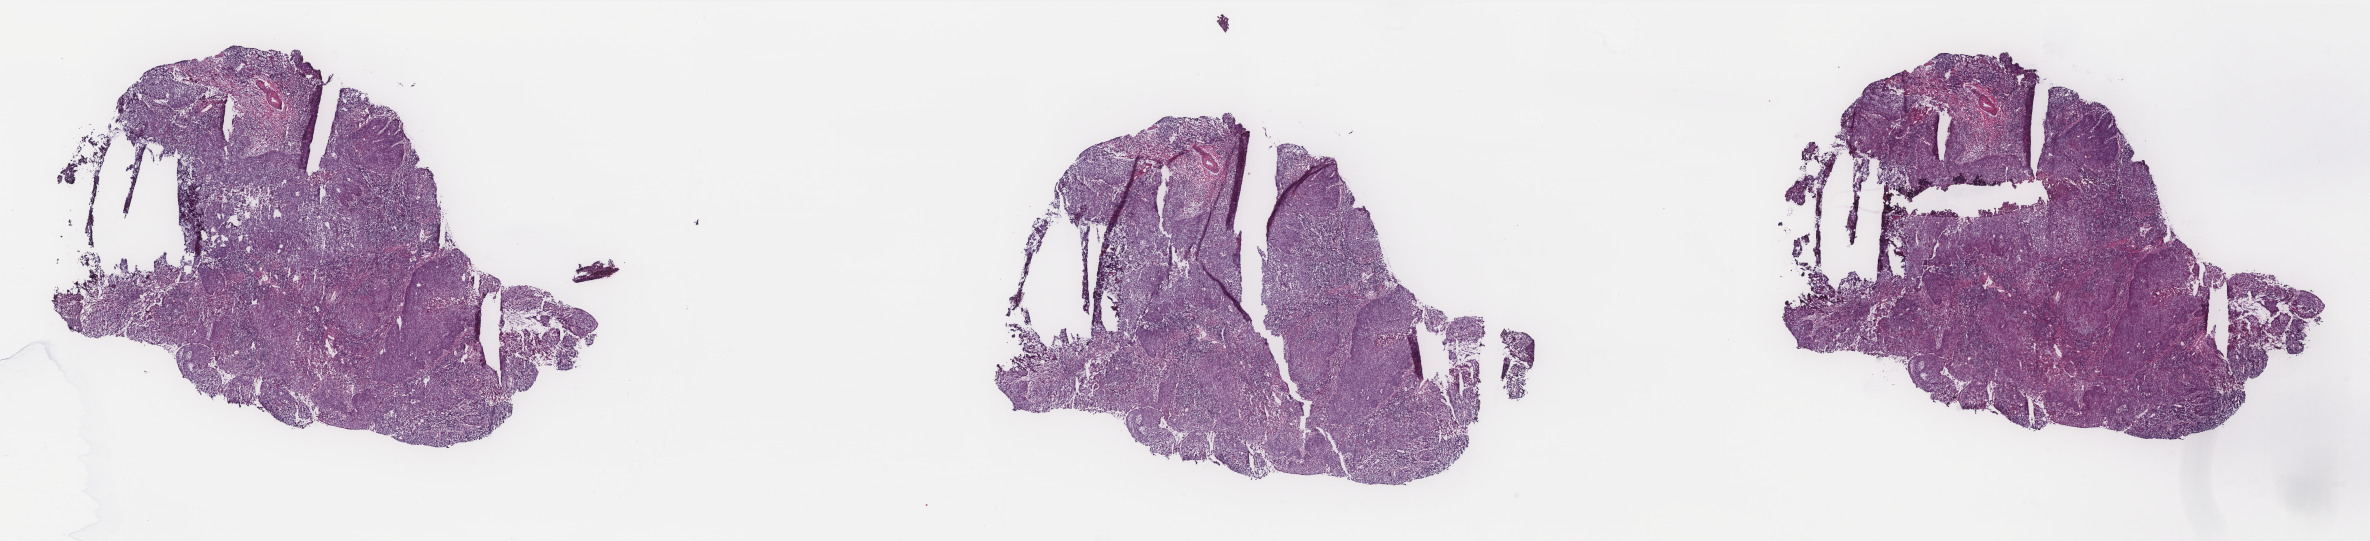
Whole-slide histology image, Hematoxylin and eosin (H&E) stained, a low-resolution overview of the entire scanned area, about 38.0 x 8.7 mm (from a 40x scan), frozen section from the top of the tissue portion, primary tumour sample from the cervix. Female patient; age at initial diagnosis 37 years. Histologic grade: G2 (moderately differentiated). Pathologist review of this section (percent, as recorded): tumour cells 58%, tumour nuclei 60%, normal cells 0%, stromal cells 40%, necrosis 2%. Infiltration values recorded for this section: lymphocyte infiltration 75%, monocyte infiltration 5%, neutrophil infiltration 5%.
FIGO stage: IB. Diagnosis: Squamous cell carcinoma, NOS. Lymph nodes positive (case pathology): 0 of 30 examined.